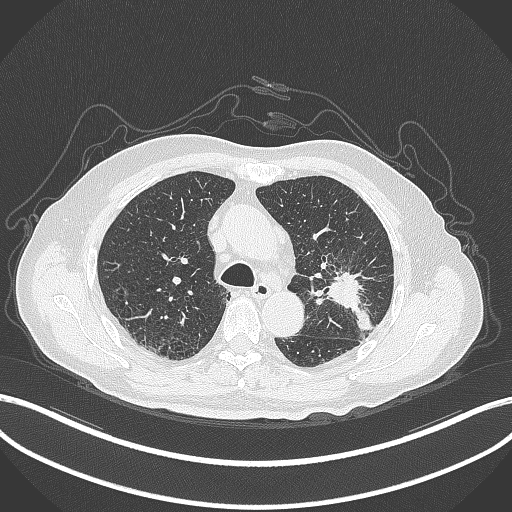
Chest CT, one axial slice. Position 197 of 331 along the scan axis. 120 kVp. Lung window (W 1500 / L -600 HU). 512 × 512 image matrix. Patient: male, 79 years. From the clinical record (not read from this slice): clinical TNM (as recorded): T2a N1 M1; histopathological grade: G3.
Annotated regions visible in this slice (rectangle marked by the reading radiologist):
- lung tumour (recorded histology: adenocarcinoma): box from (x=321, y=268) to (x=373, y=336) px